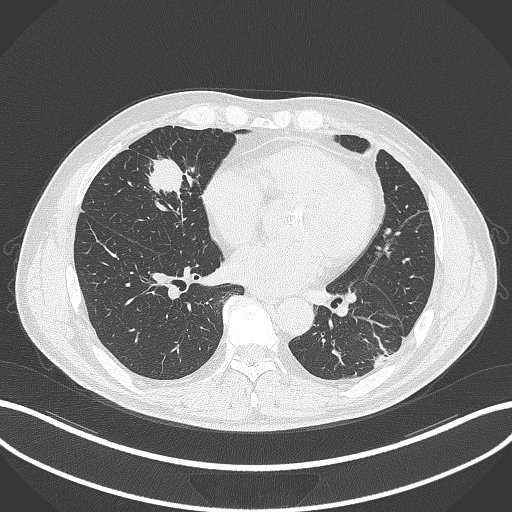
Chest CT, one axial slice. Position 115 of 399 along the scan axis. 120 kVp. Lung window (W 1500 / L -600 HU). 1 mm slice thickness. 512 × 512 image matrix, field of view 400 × 400 mm. Male patient, age 59 years. From the clinical record (not read from this slice): clinical TNM (as recorded): T2a N1 M0.
Annotated regions visible in this slice (bounding box drawn by a radiologist):
- lung tumour (recorded histology: adenocarcinoma): bounding box [x1, y1, x2, y2] px = [142, 157, 186, 200]